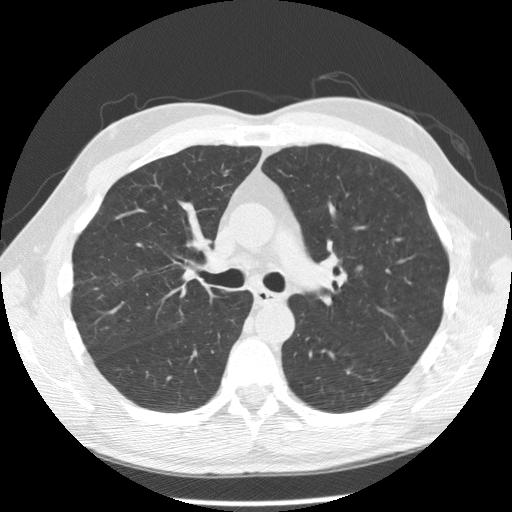
Chest CT (low-dose screening protocol), one axial image, second screening round (one year after baseline), lung window (W 1500 / L -600 HU), 2.5 mm slice thickness, 512 × 512 image matrix, field of view 350 × 350 mm. Male participant, aged 55 years at enrolment. Current smoker at enrolment.
Lesion marked by an expert reader, bounding box (x1, y1, x2, y2) in pixels: (332, 251, 377, 294). Screening reader's record for this exam: no non-calcified nodule ≥4 mm recorded. Lung cancer was diagnosed 356 days after this screen (after the third annual screen): small cell carcinoma, NOS, left upper lobe, undifferentiated (G4), stage IV (AJCC 6th edition), 60 mm at pathology.